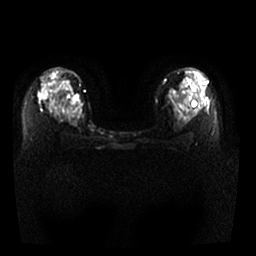
Breast MRI, one axial slice. Position 20 of 29 along the scan axis. Diffusion-weighted series; image 2 of 4 stored at this slice position (different b-values; order by instance number). 1.5 T. 4 mm slice thickness. 256 × 256 image matrix. Female patient.
Outlined on this slice (manually delineated by an expert):
- tumour on diffusion-weighted imaging: box from (x=71, y=95) to (x=79, y=105) px